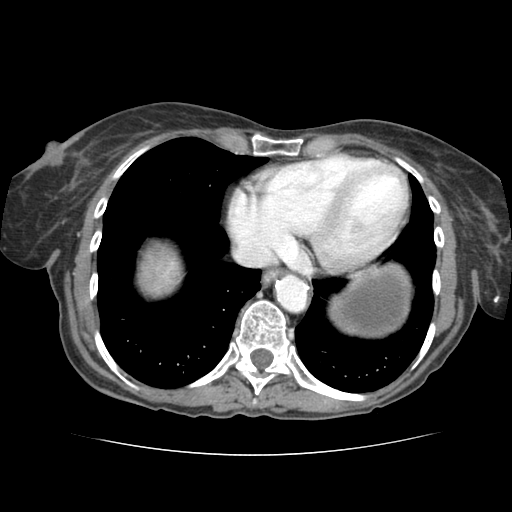
Contrast-enhanced abdominal CT (liver protocol), one axial slice. Position 75 of 77 along the scan axis. Reconstruction kernel STANDARD. Soft-tissue window (W 400 / L 40 HU). 2.5 mm slice thickness. 512 × 512 image matrix, field of view 340 × 340 mm. Case-level facts recorded for this patient, not image findings: diagnosis: hepatocellular carcinoma (patient treated with transarterial chemoembolisation; whether this scan precedes or follows treatment is not stated here); TNM stage (as recorded): Stage-I; Child-Pugh class: A; tumour nodularity: uninodular; tumour size: 7.6 cm.
Structures marked on this image (semi-automatically segmented with operator editing):
- liver parenchyma outside the tumour (the mass and vessels are separate outlines, so this box may not span the whole liver): bounding box <148,252,172,276> (left, top, right, bottom; pixels)